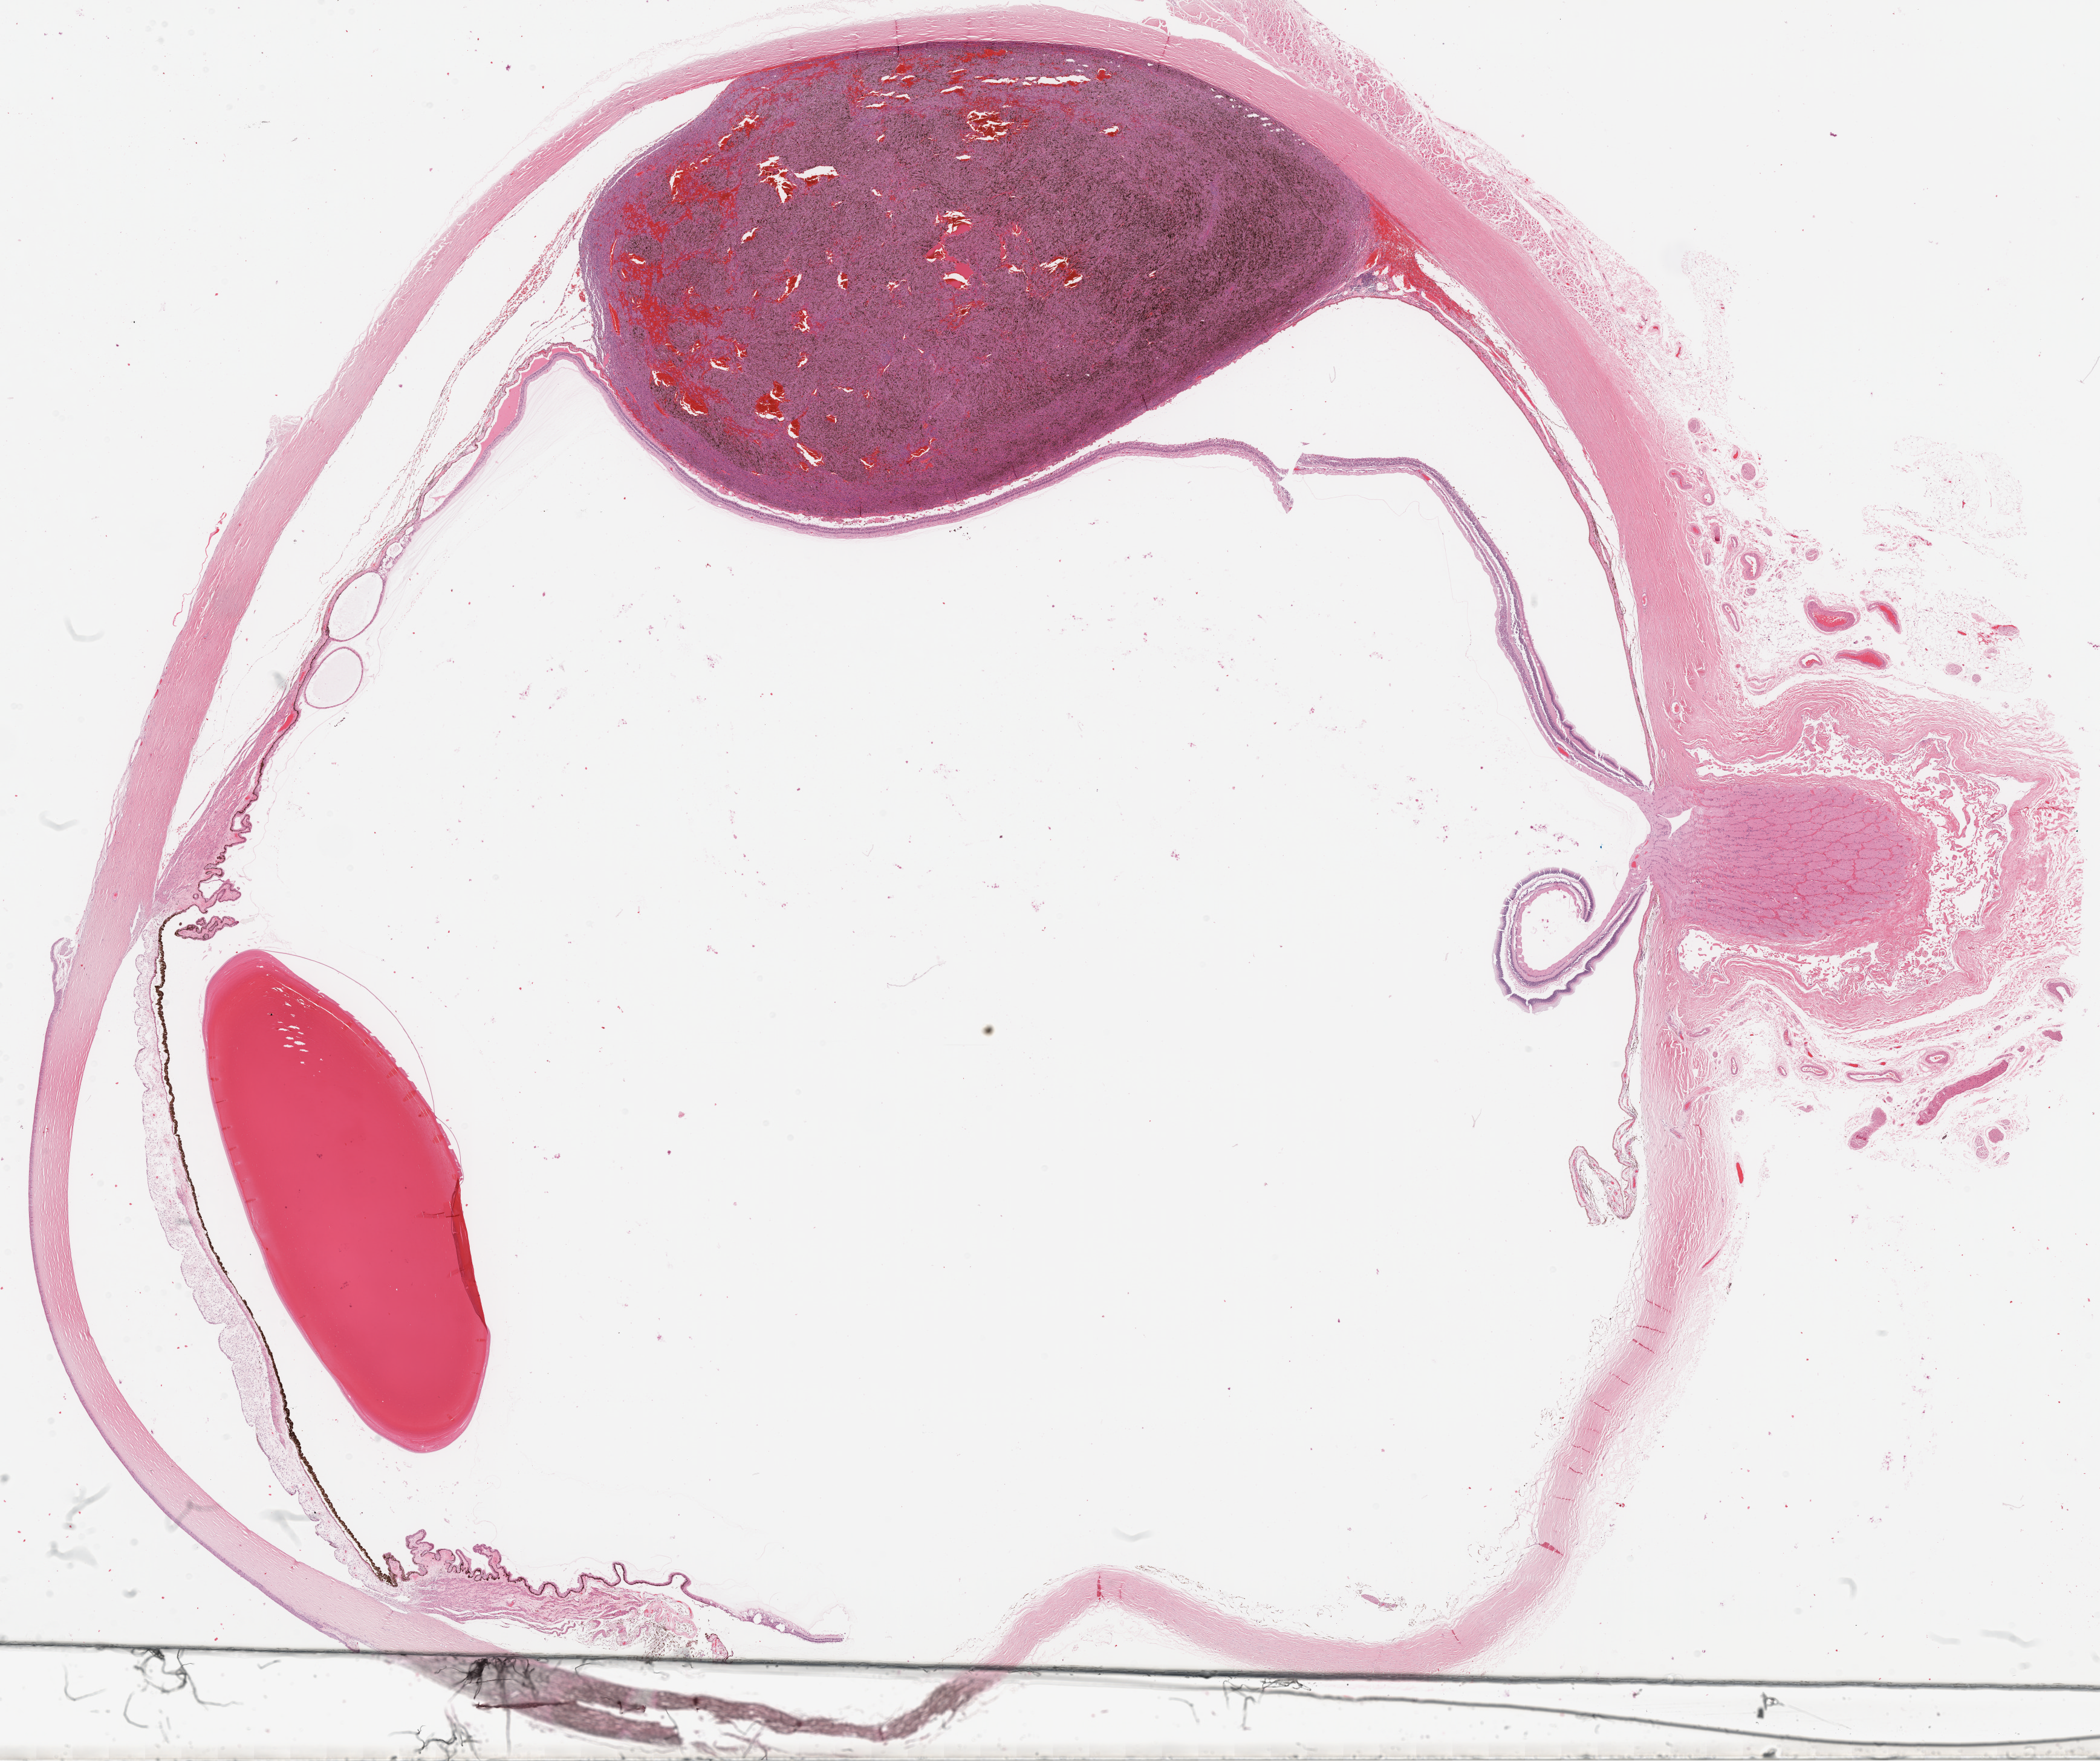
Whole-slide histology image, Hematoxylin and eosin (H&E) stained — shown as a low-resolution overview of the whole scanned area (about 28.0 x 23.5 mm, acquisition: 20x scan), formalin-fixed paraffin-embedded (FFPE) diagnostic section, sample: primary tumour, uvea. Male patient; age at initial diagnosis 65 years. Pathologist review of this section (percent, as recorded): tumour cells 50%, tumour nuclei 60%, normal cells 50%, stromal cells 0%, necrosis 0%. Inflammatory infiltration, as recorded: lymphocyte infiltration 1%, monocyte infiltration 0%, neutrophil infiltration 0%.
• AJCC pathologic stage: IIB (7th edition)
• histologic diagnosis: Mixed epithelioid and spindle cell melanoma (choroid)